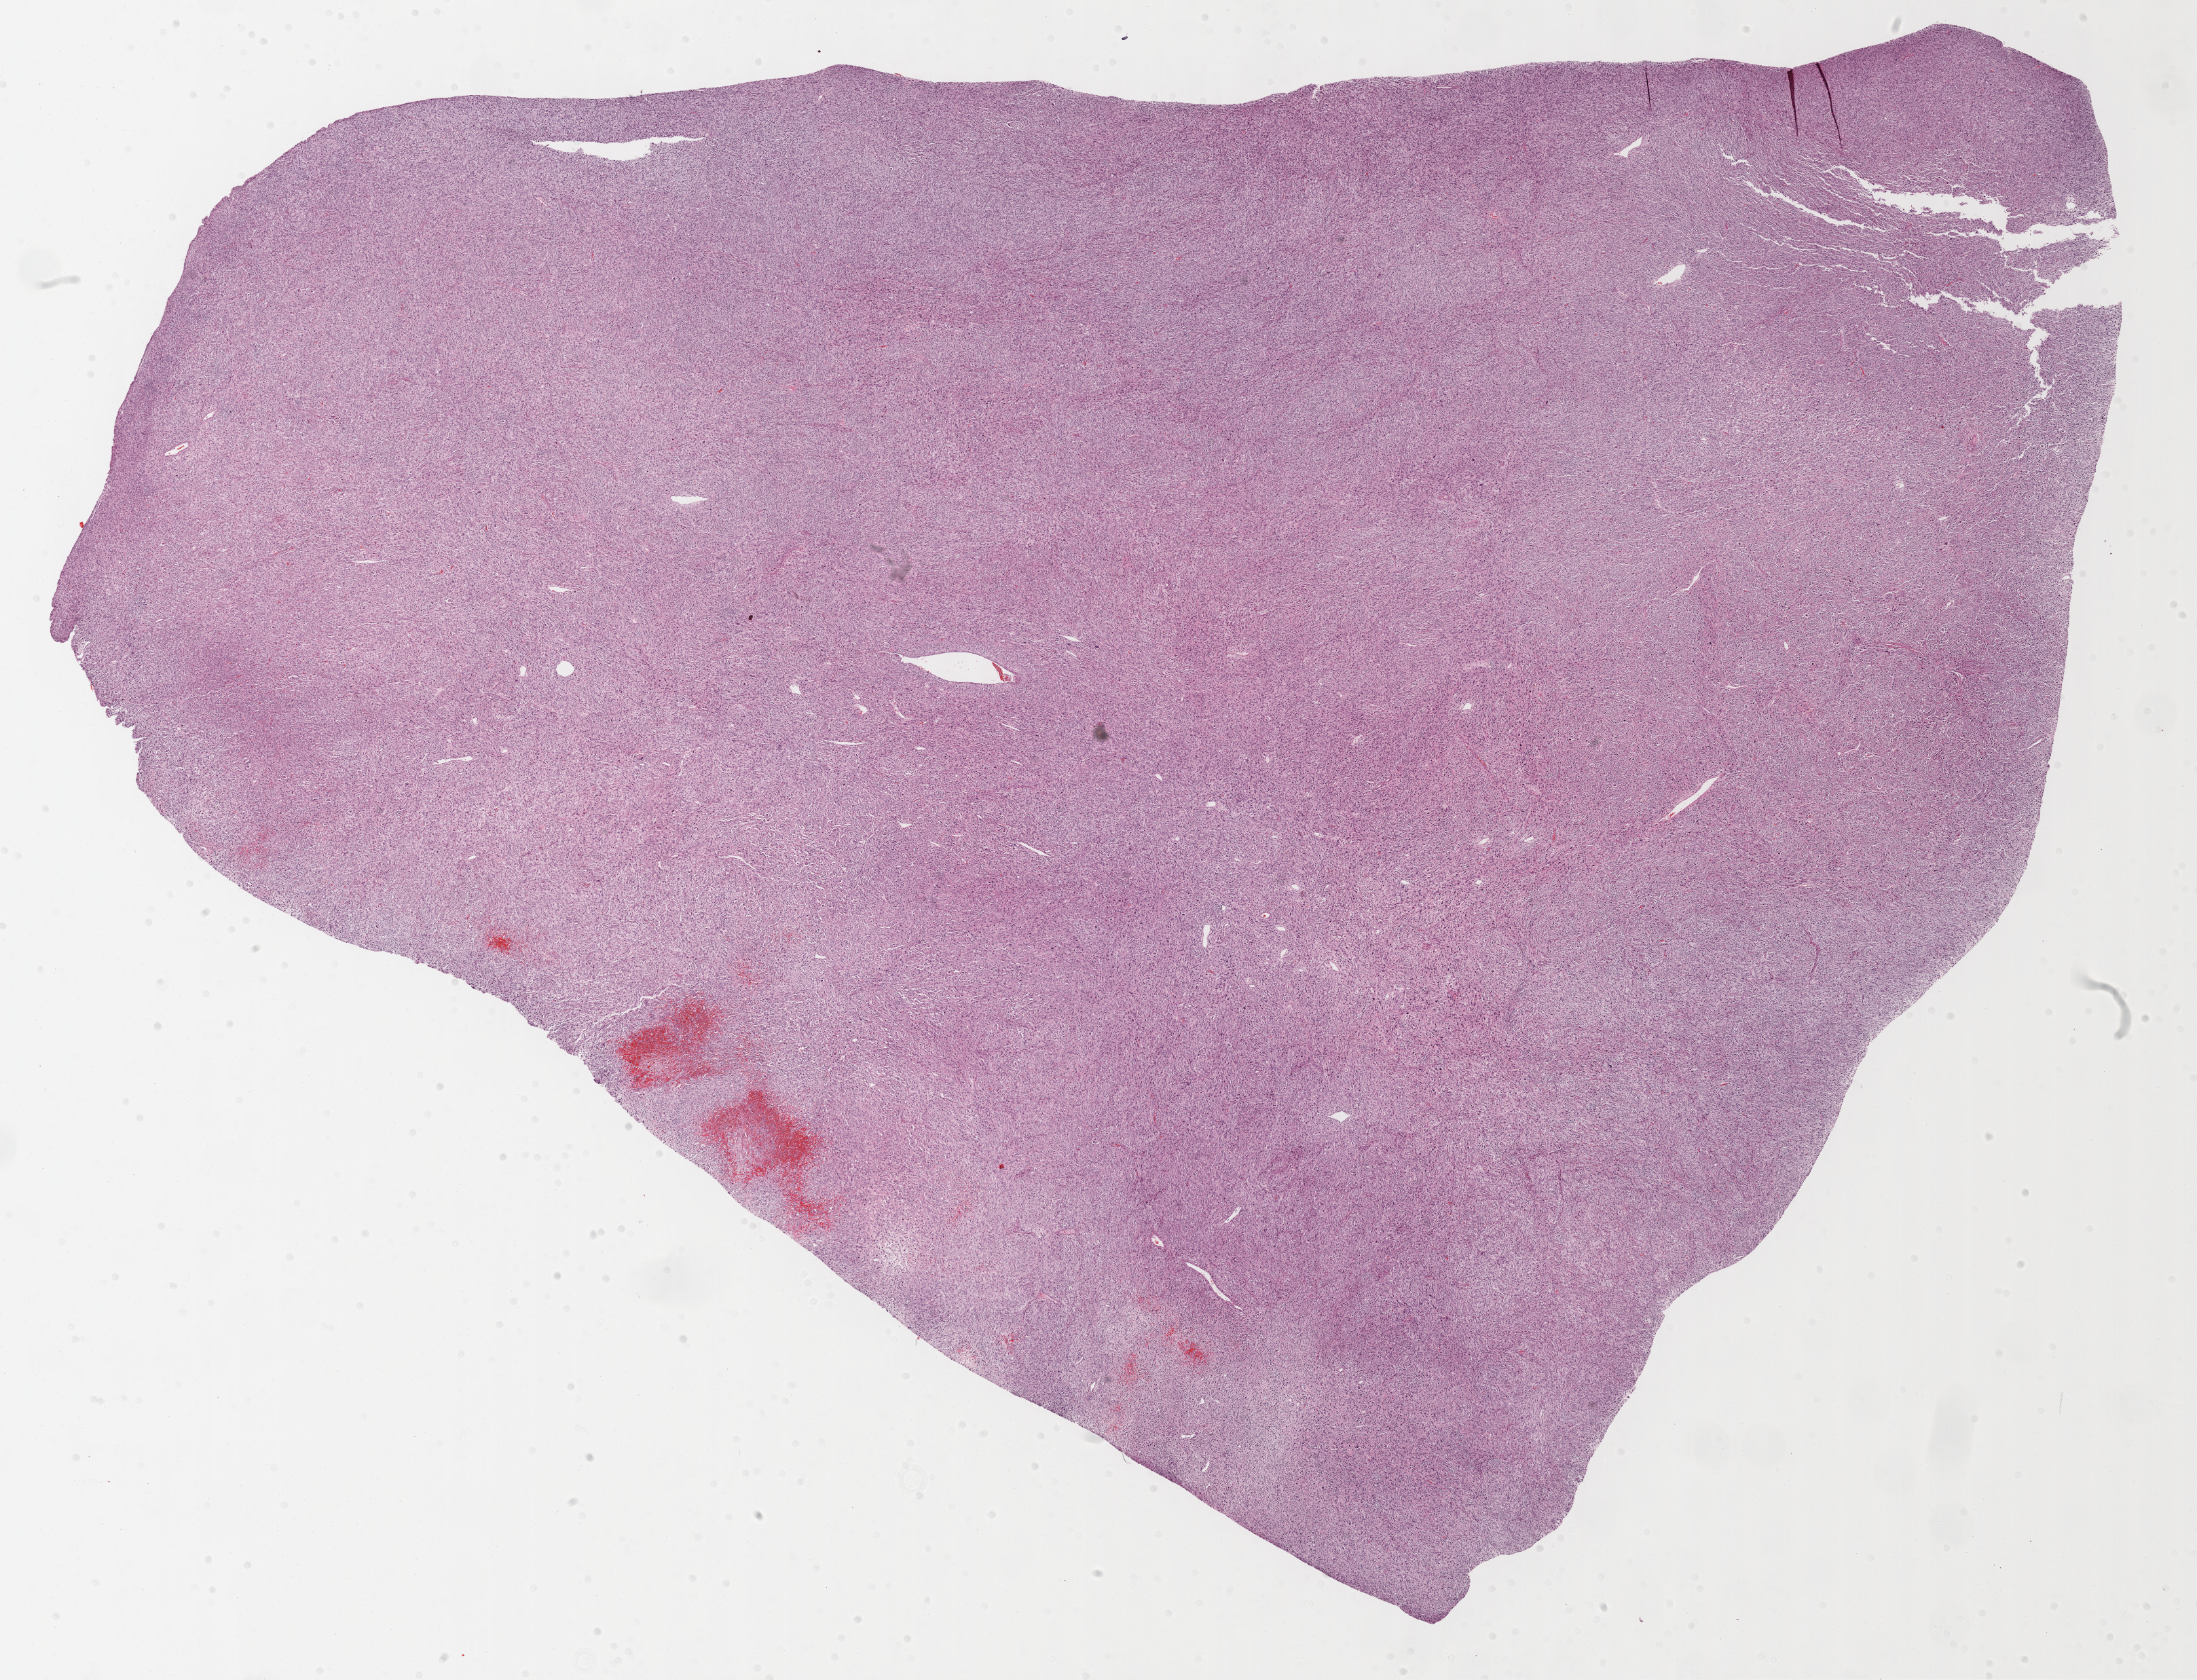
H&E whole-slide image, whole scanned area (about 26.2 x 20.0 mm, slide scanned at 40x) shown as a low-resolution overview. FFPE section. Sample: primary tumour, connective, subcutaneous and other soft tissues. Patient: female, age at initial diagnosis 61 years.
Pathologic diagnosis: Undifferentiated sarcoma.